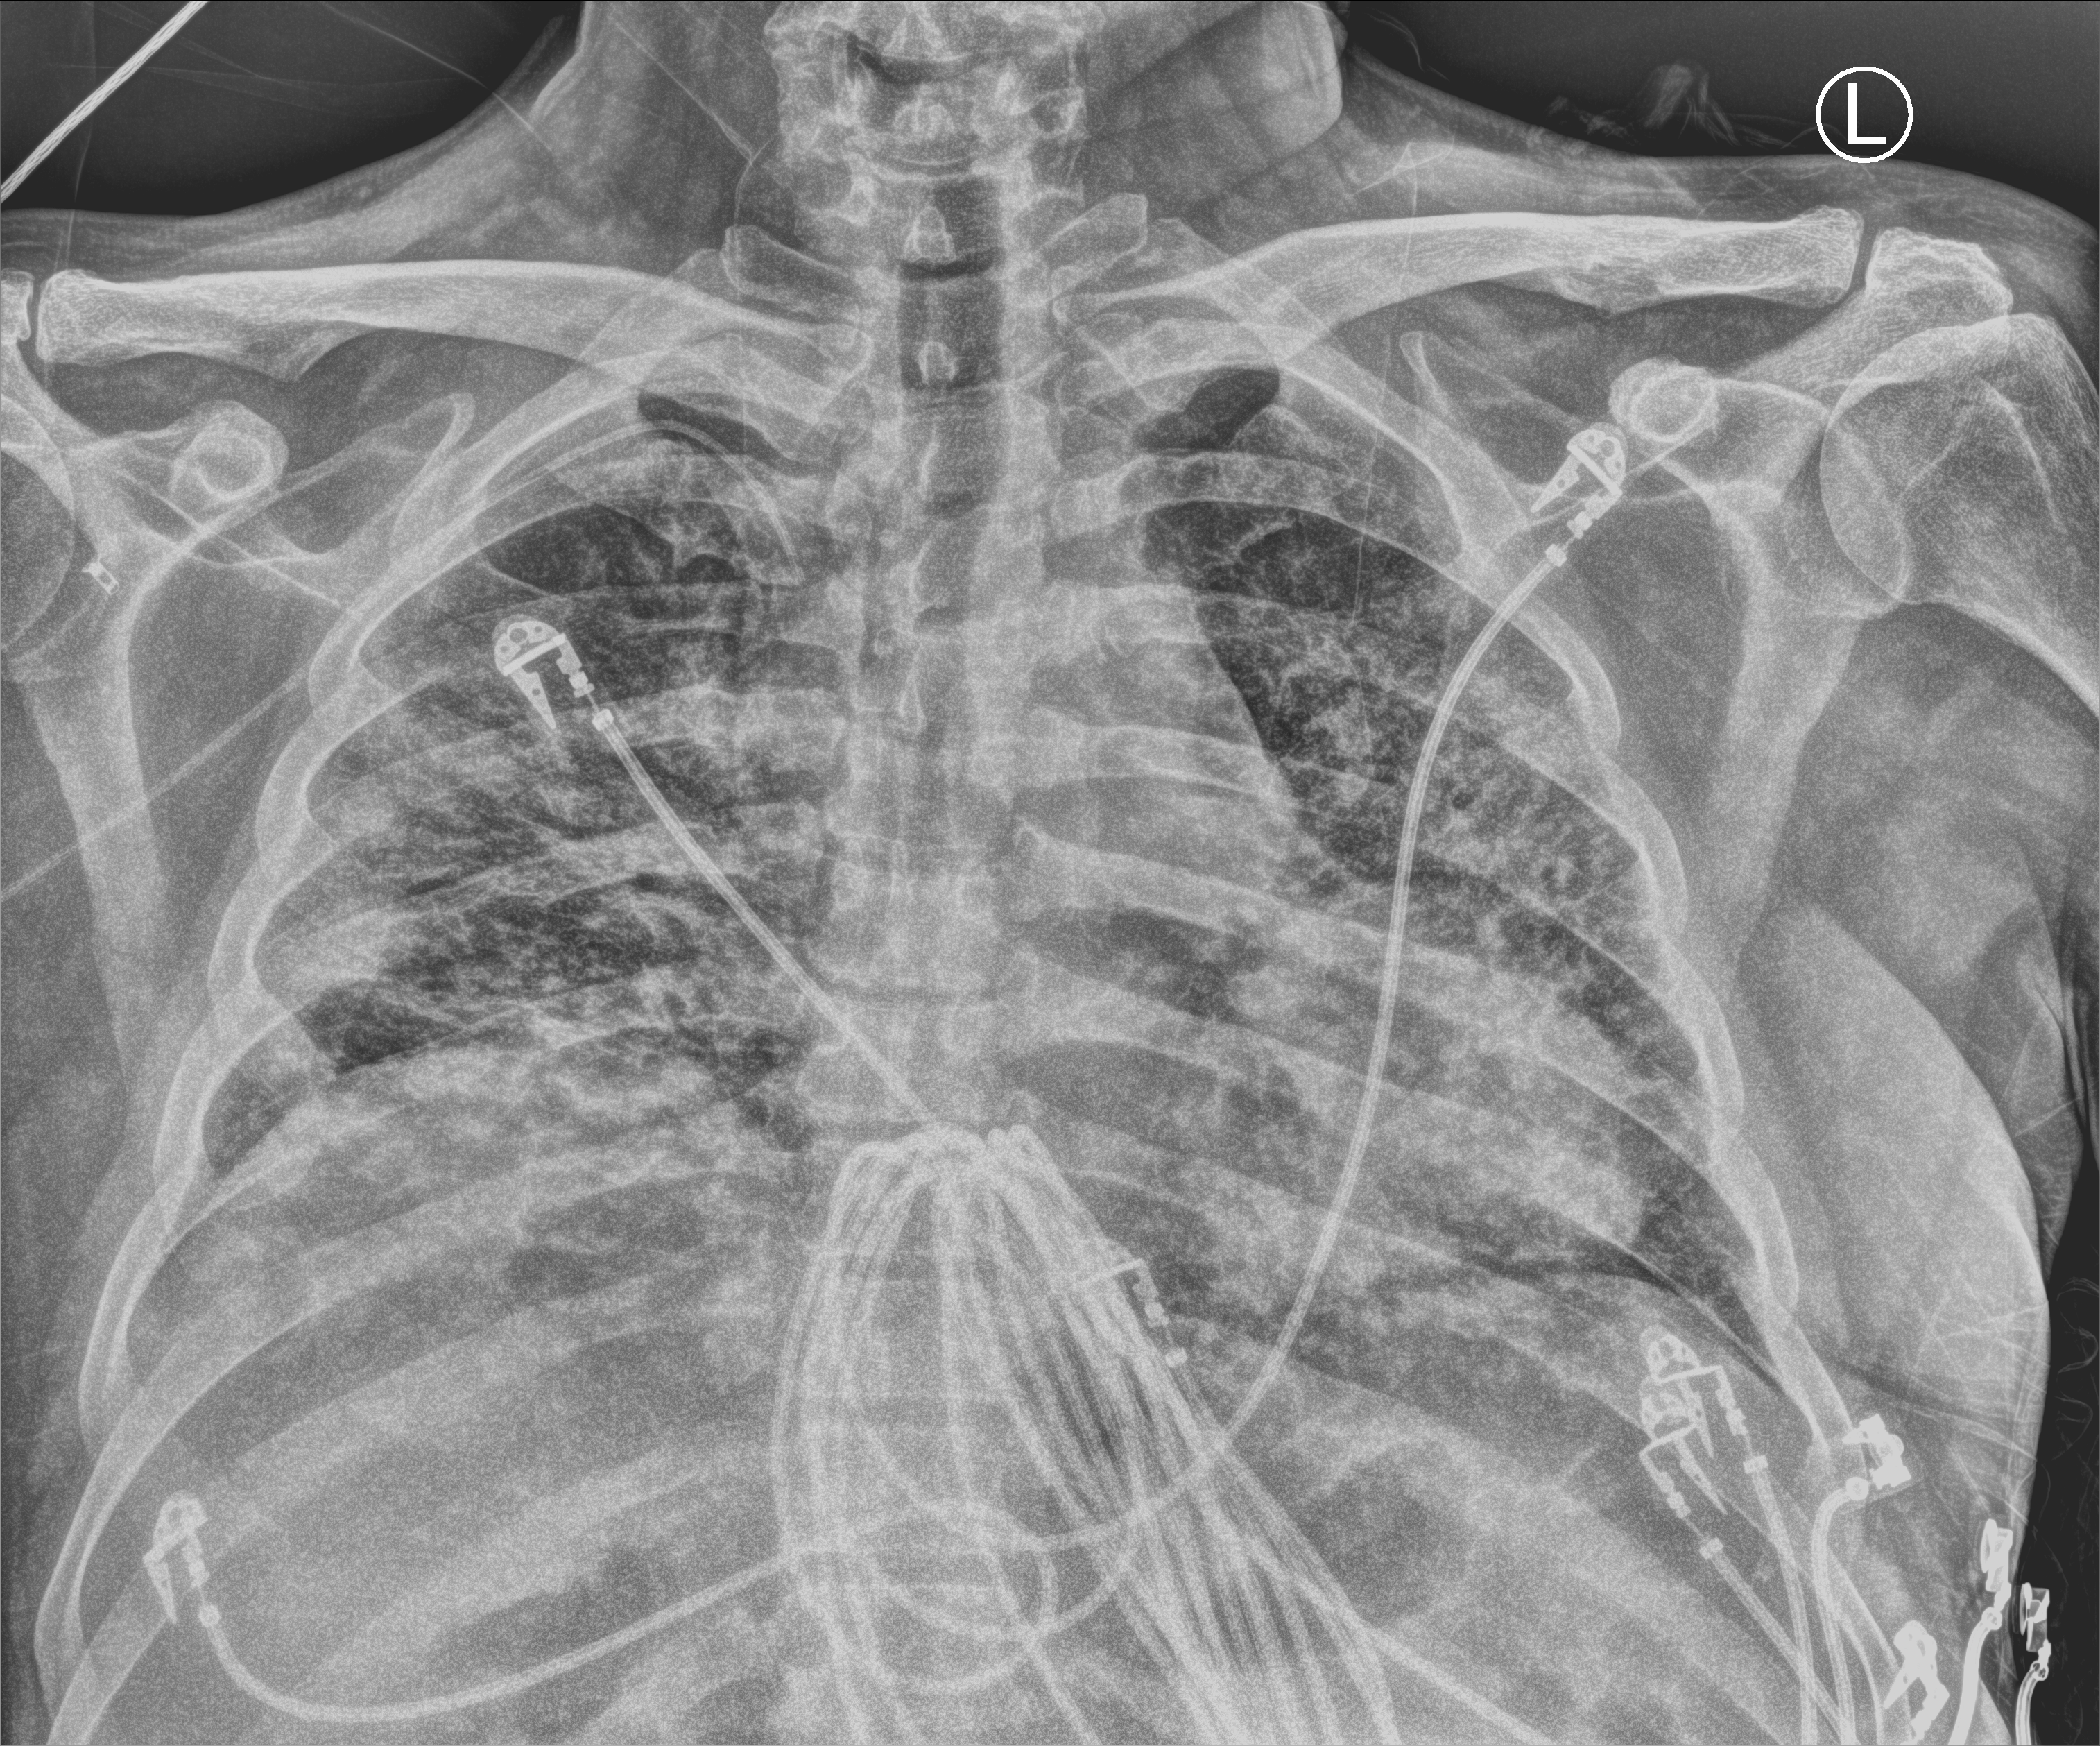
Chest X-ray (portable). Patient hospitalised with COVID-19; male, aged 18–59 years.
From the hospital-stay record, not from the radiograph (when in the stay this image was taken is not recorded): admitted to intensive care during this hospital stay: yes; mechanically ventilated during this hospital stay: yes.